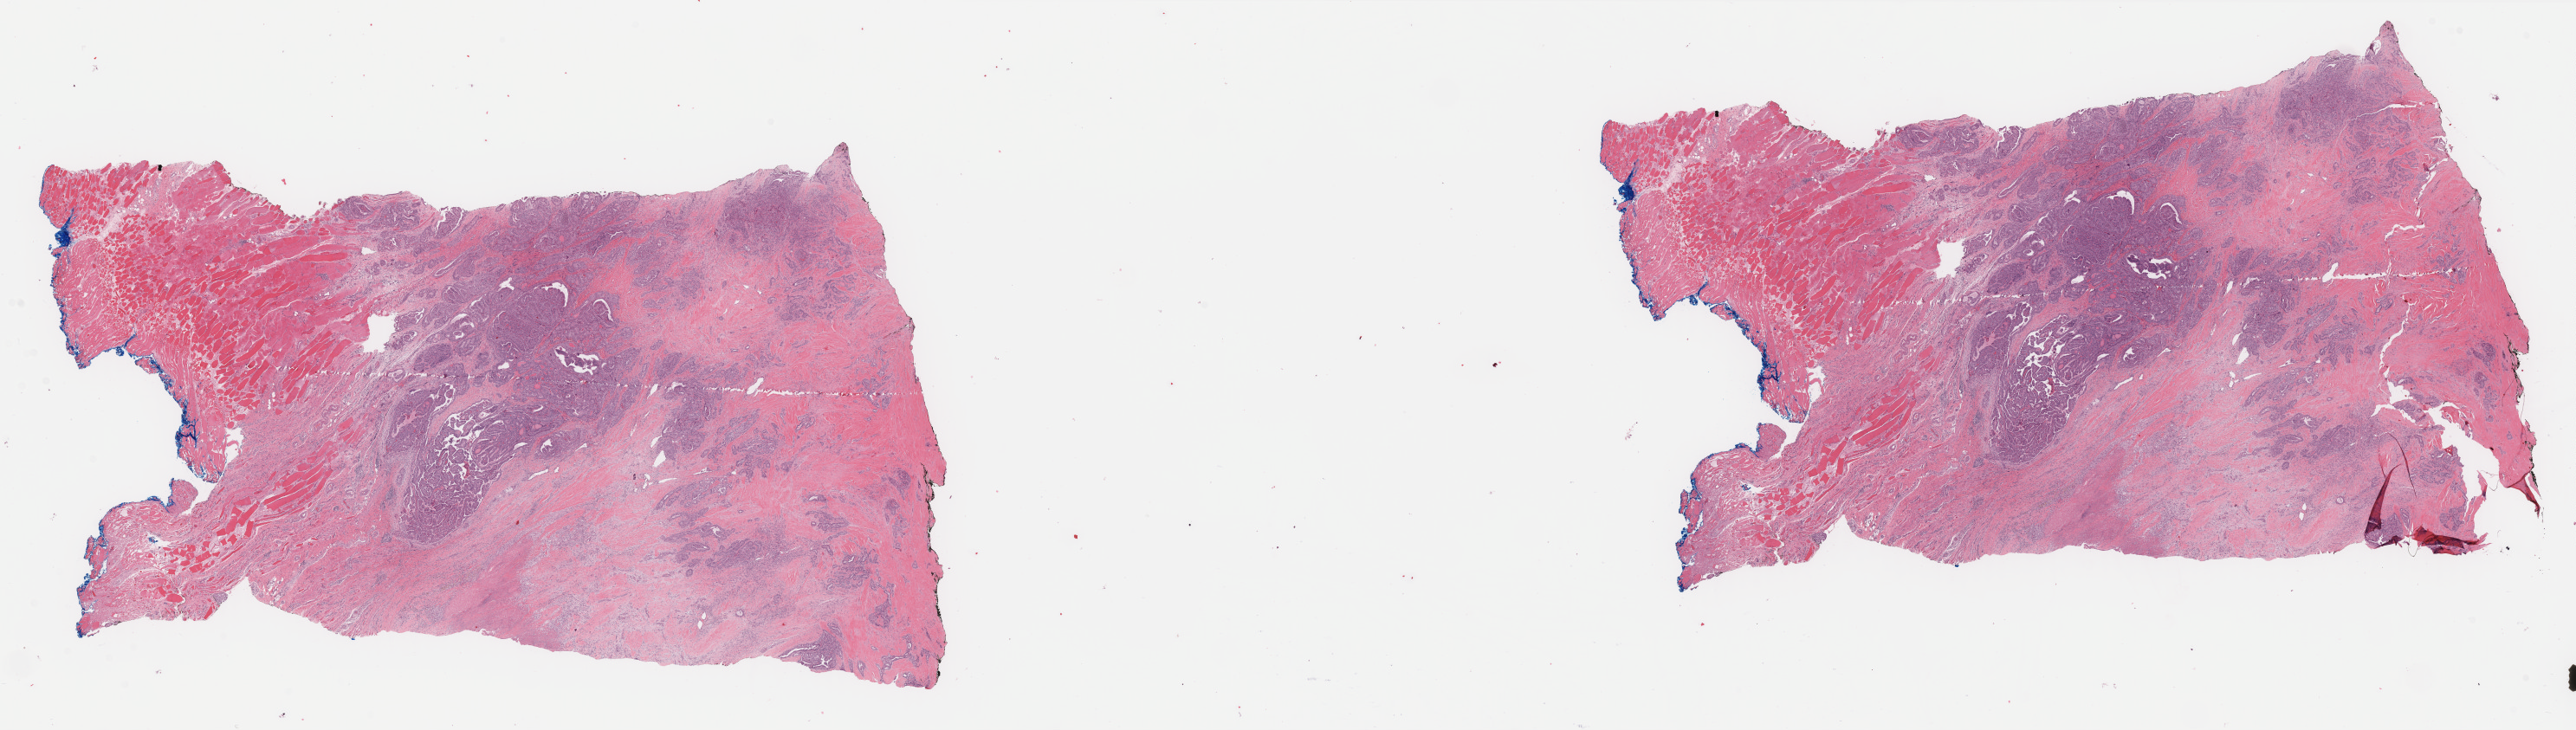
Whole-slide histology image, Hematoxylin and eosin (H&E) stained — low-resolution overview of the scanned area, about 47.1 x 13.3 mm (slide scanned at 40x); formalin-fixed paraffin-embedded (FFPE) diagnostic section; thyroid, primary tumour sample. Female, age 79 years at initial diagnosis.
TNM: T3 N1b M0. Histologic diagnosis: Papillary adenocarcinoma, NOS (thyroid gland). AJCC pathologic stage: IVA. Lymph nodes positive (case pathology): 3 of 36 examined.